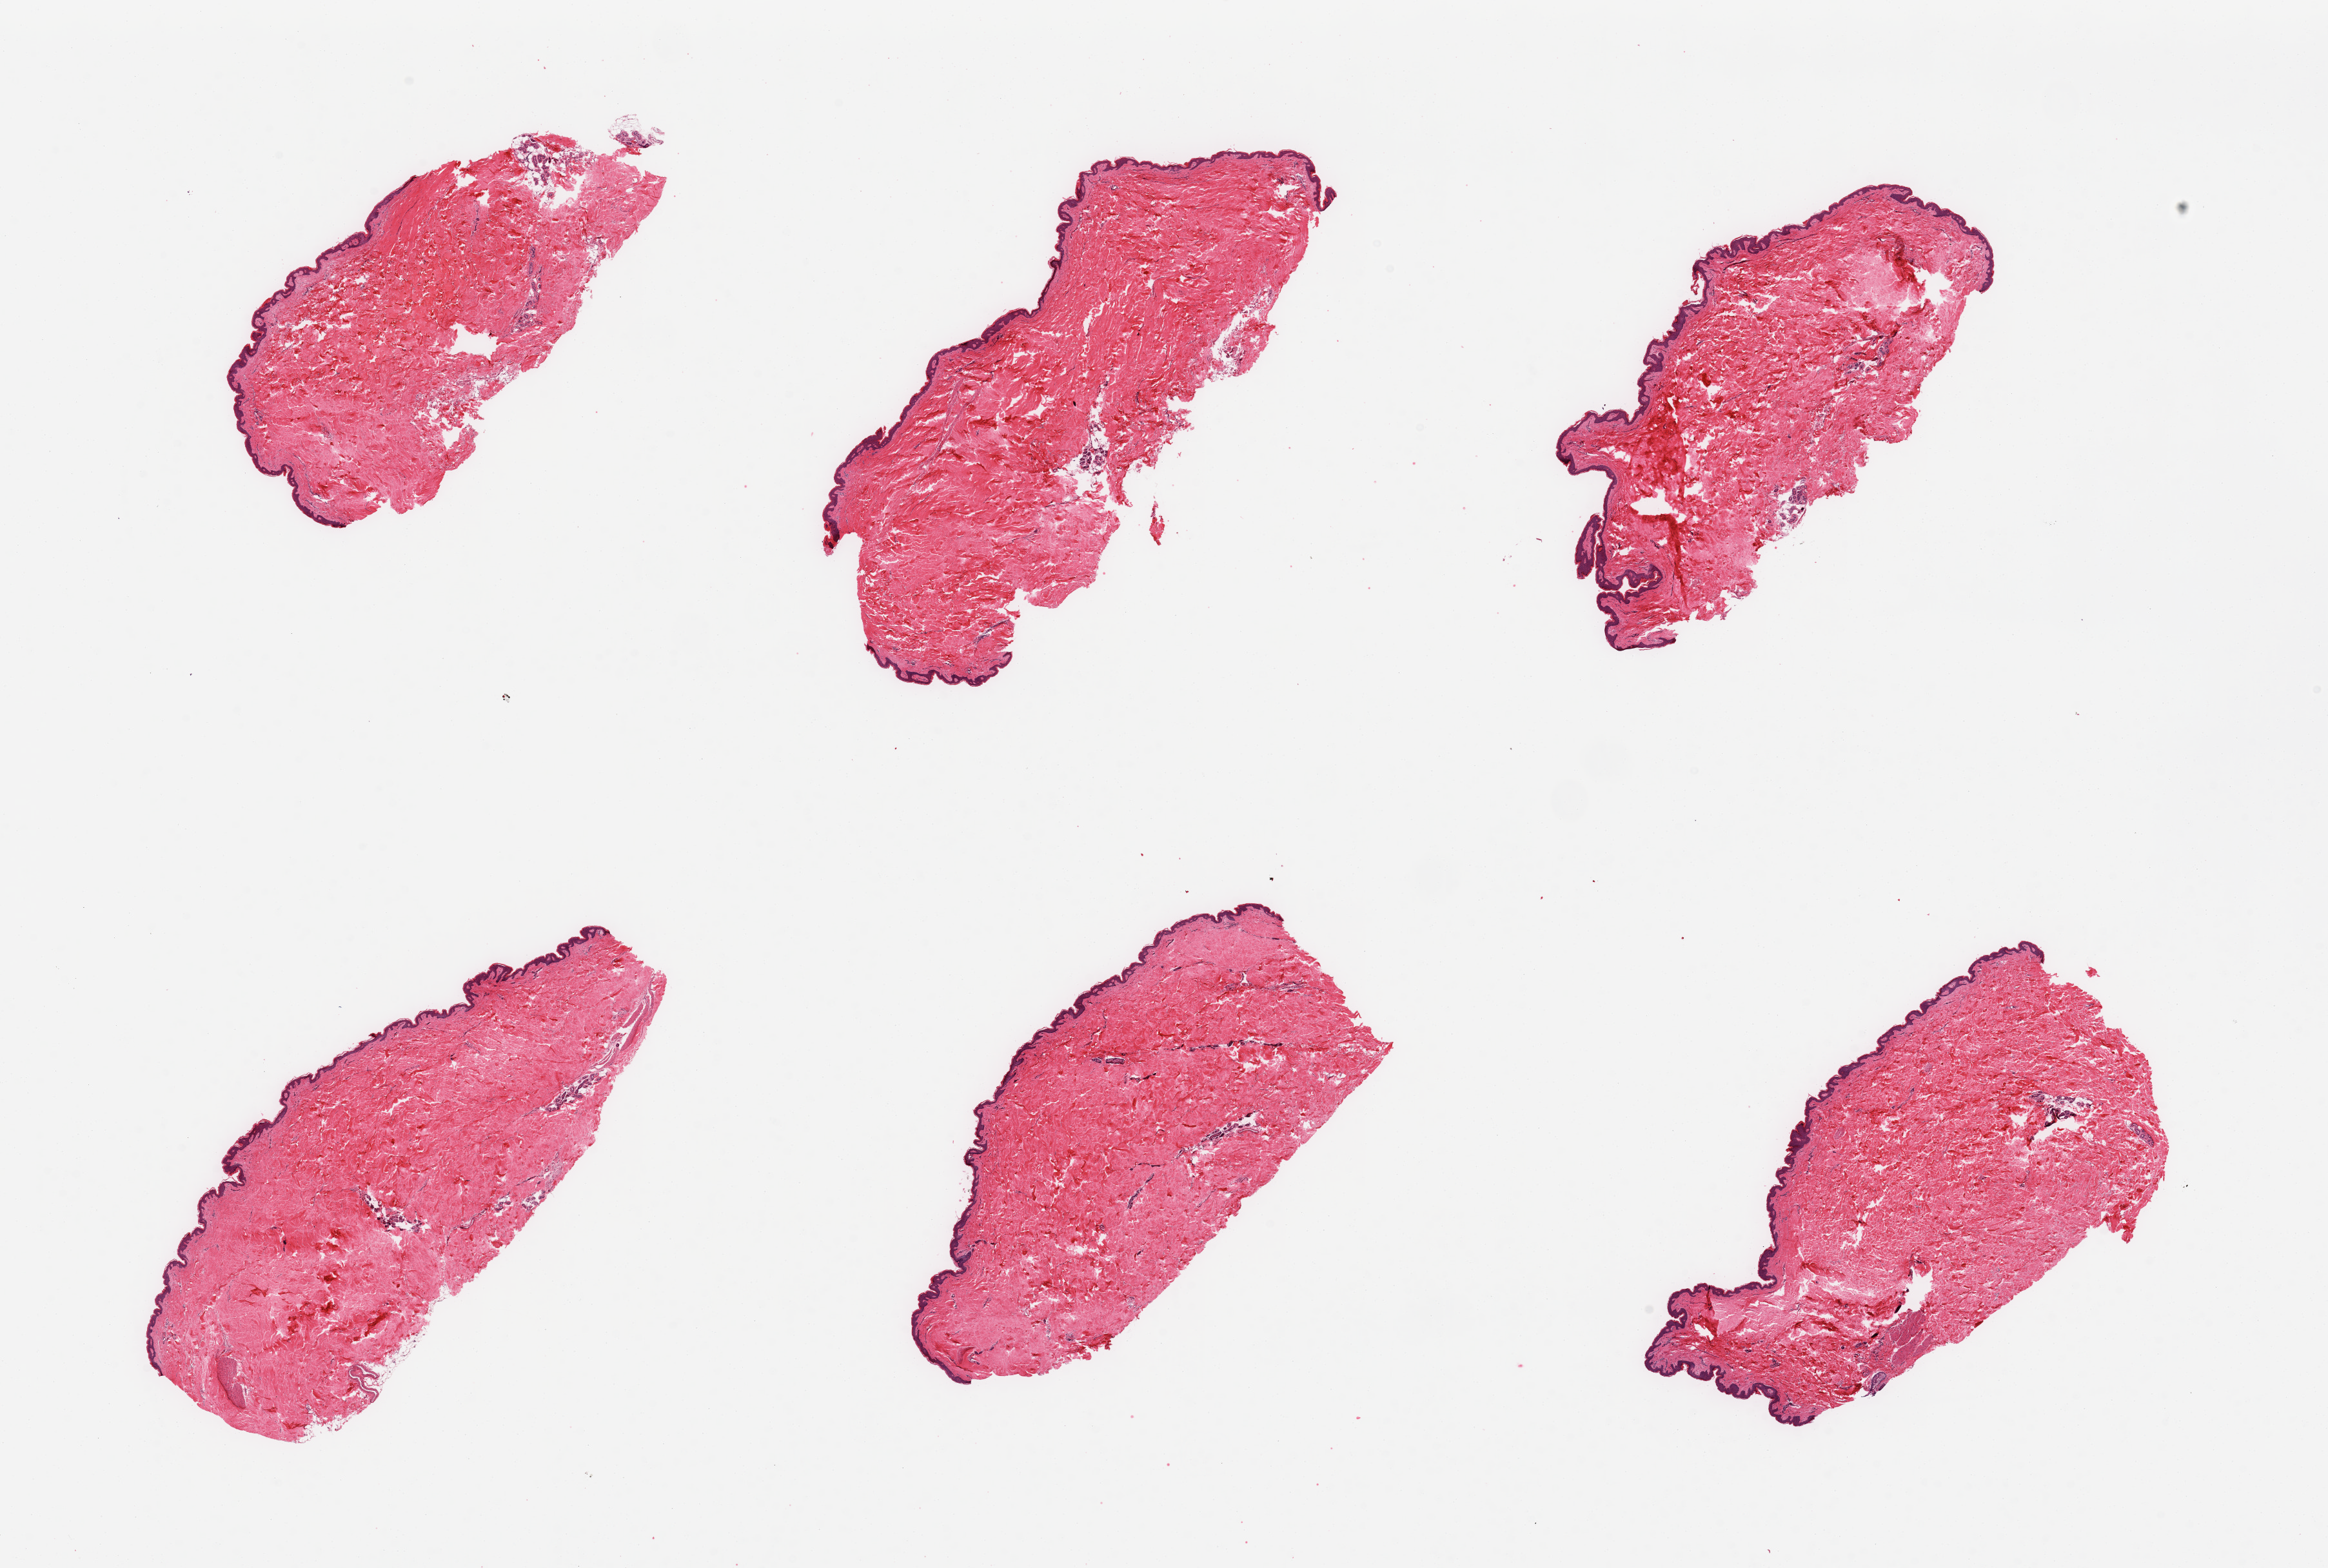
Whole-slide image, H&E stain, brightfield — low-resolution overview of the scanned area, about 28.5 x 19.2 mm (slide scanned at 20x), PAXgene-fixed paraffin-embedded (PFPE) section, section of skin of suprapubic region (target tissue), tissue donor sample. Female donor.
* pathologist's review note for this sample: 6 pieces; well trimmed, minimal fat